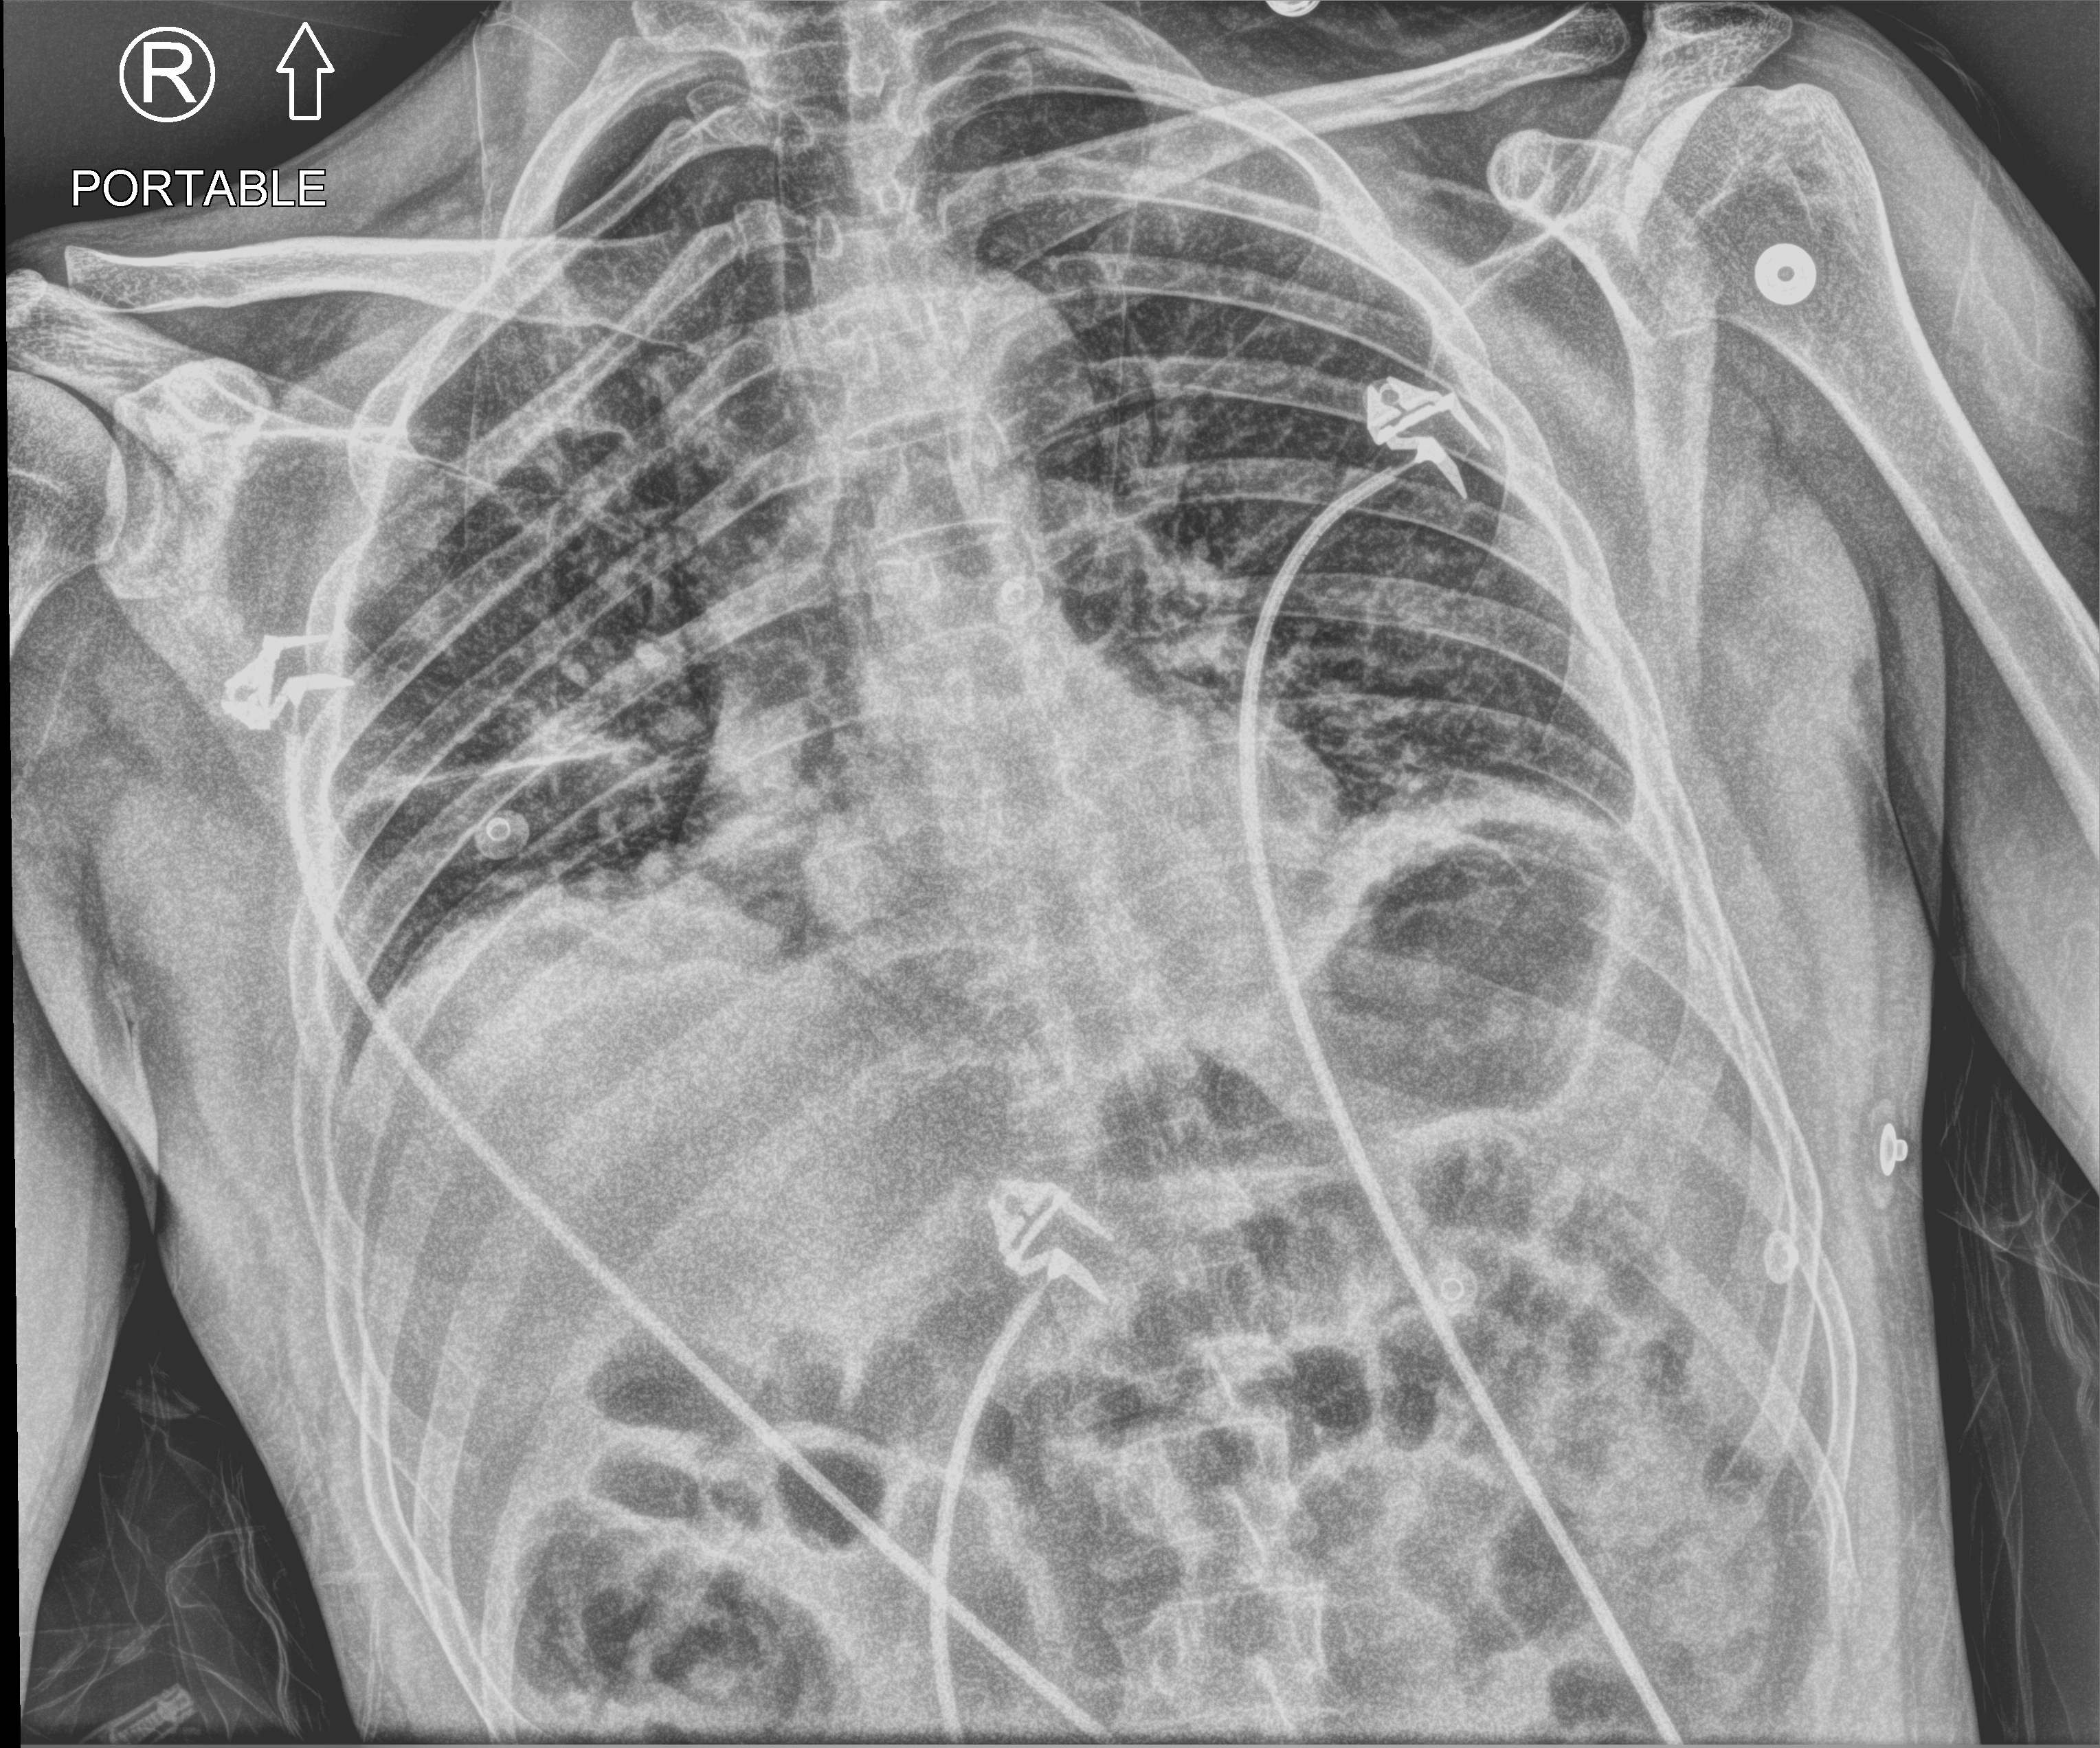
Chest X-ray (portable); anteroposterior (AP) projection. Patient hospitalised with COVID-19; male, aged 18–59 years.
Hospital-stay facts (about this admission, not read from this image; timing relative to this image not recorded):
- mechanically ventilated during this hospital stay: no